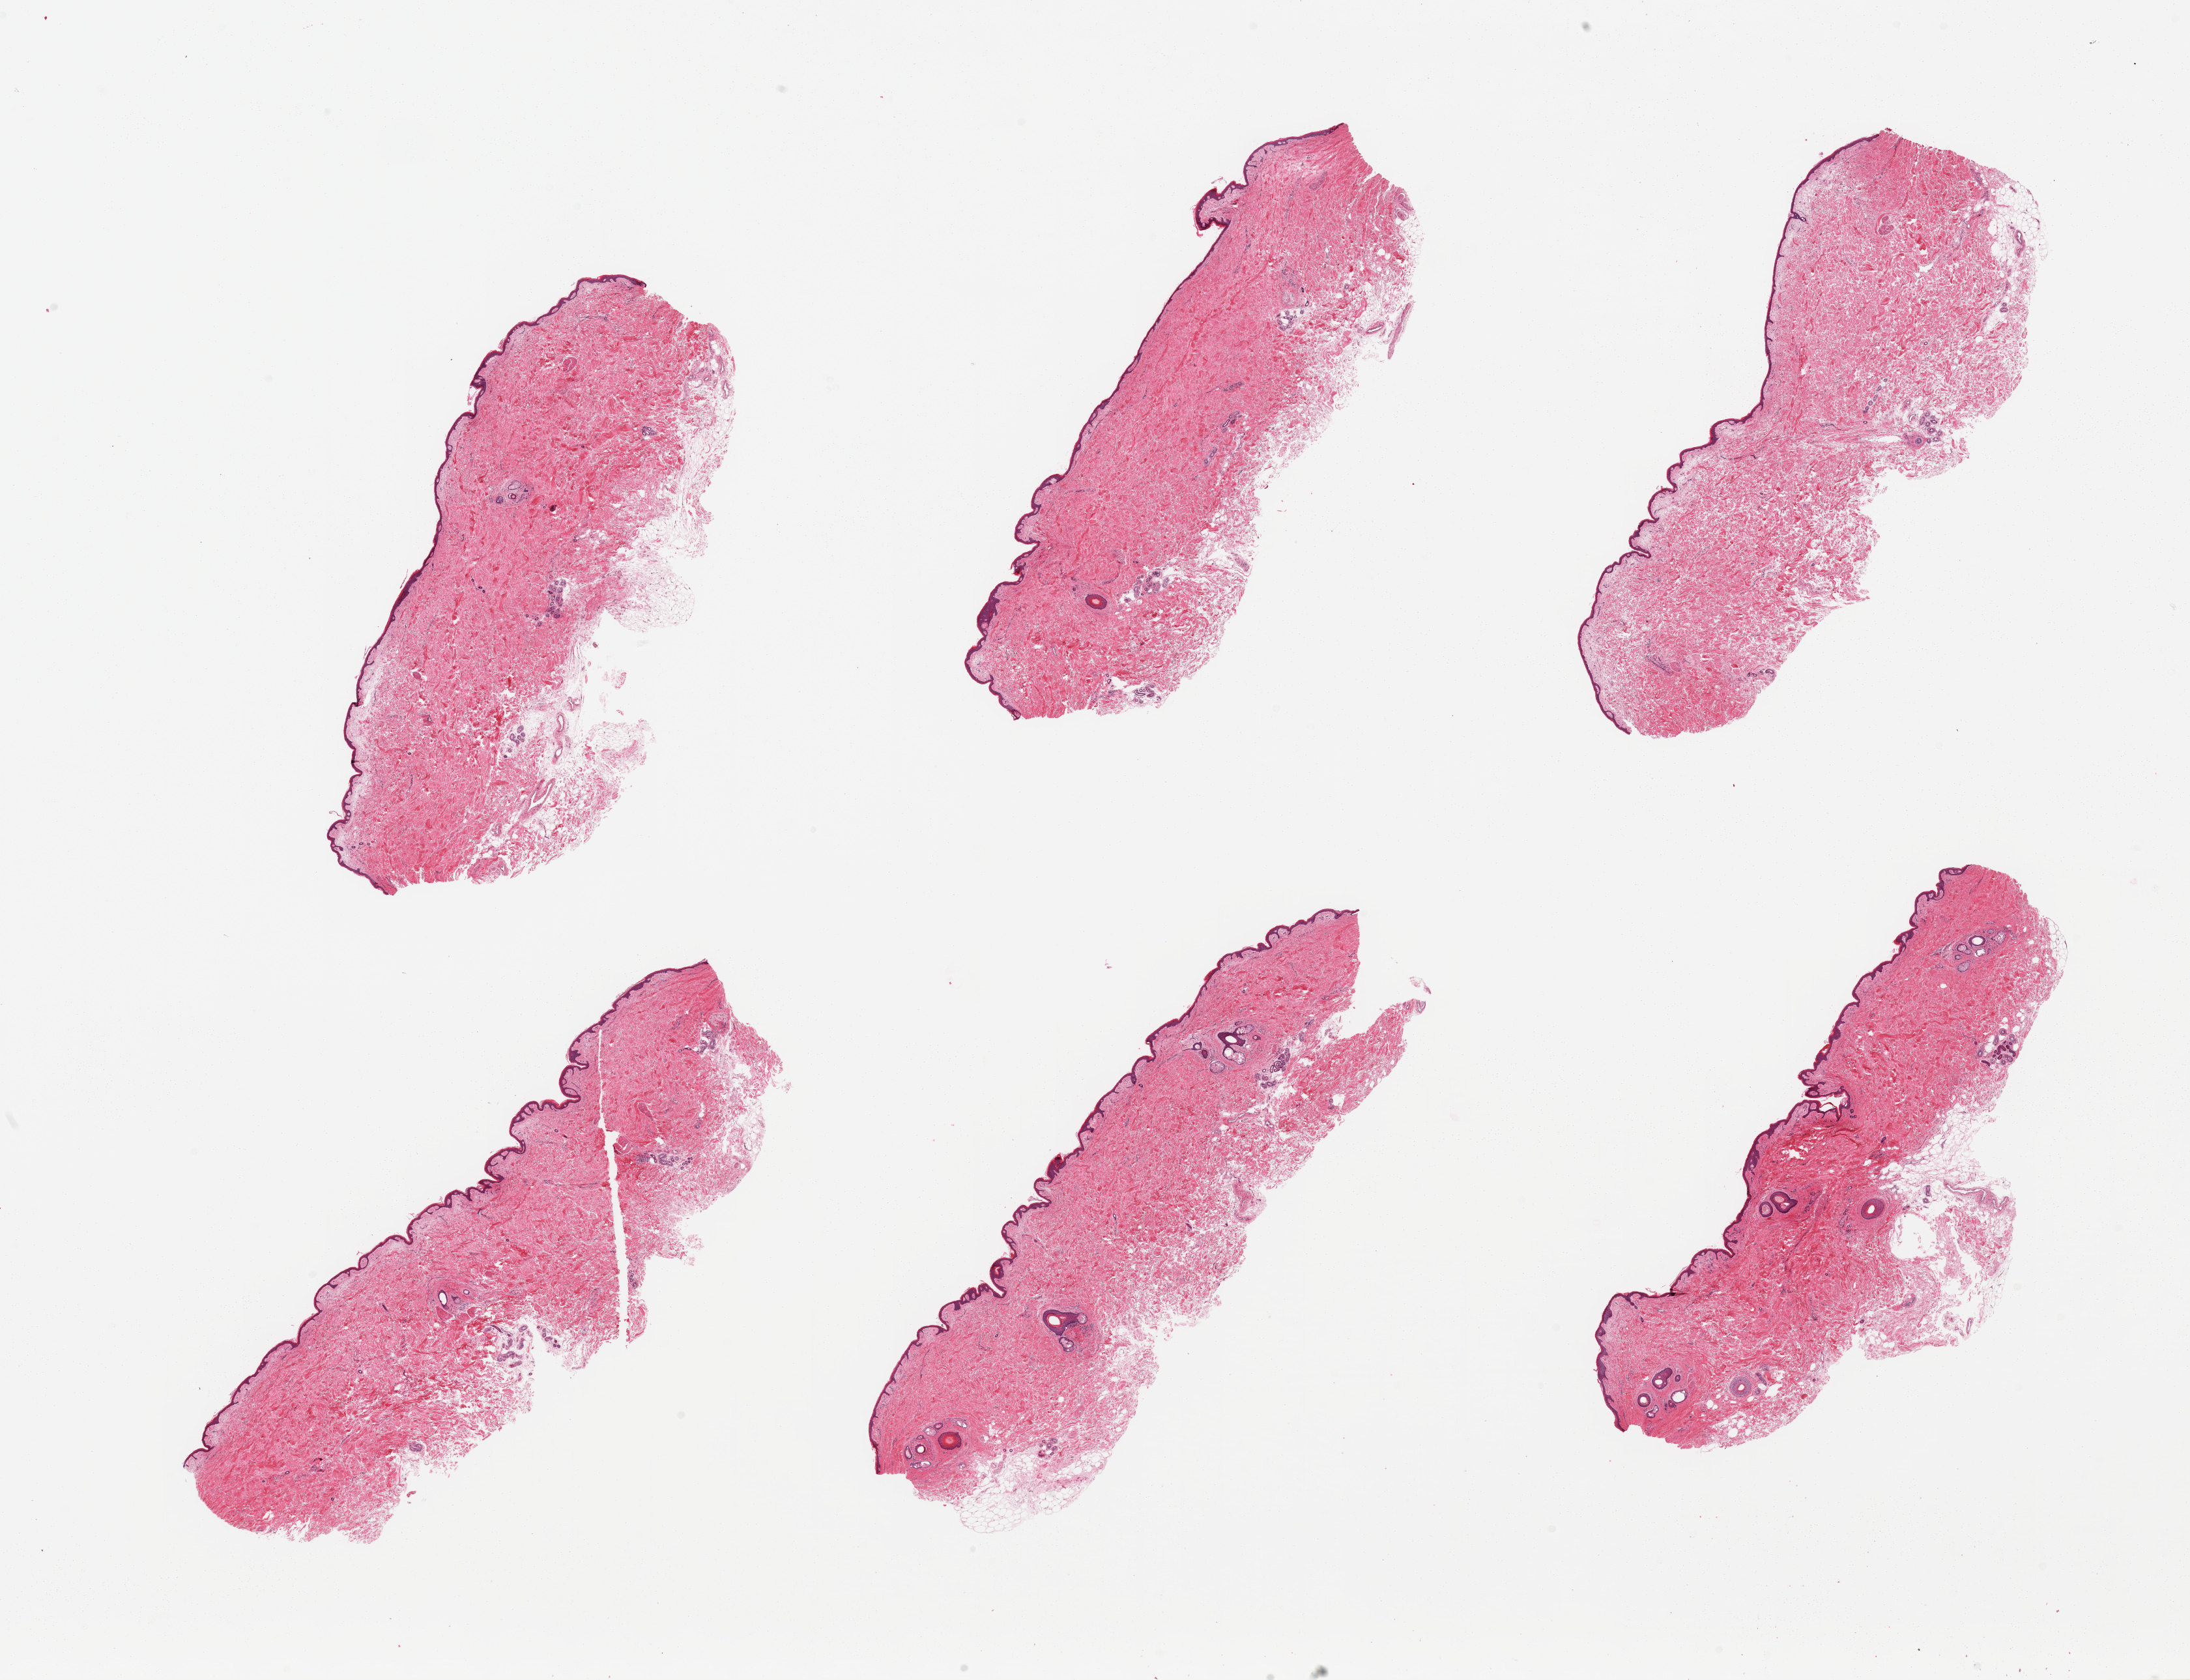
Digitized hematoxylin and eosin (H&E)-stained section, brightfield — shown as a low-resolution overview of the whole scanned area (about 26.6 x 20.4 mm, from a 20x scan); PAXgene-fixed, paraffin-embedded tissue; section of skin of suprapubic region (target tissue); tissue donor sample.
• review note (as recorded): 6 pieces, up to ~1mm dermal fat; squamous epithelium is ~20-25microns